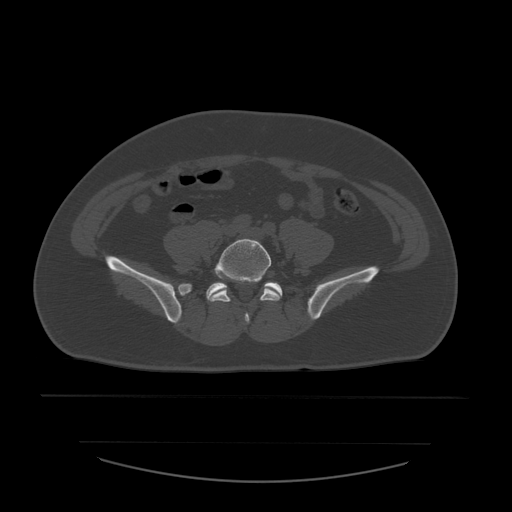
CT including the spine, one axial slice; position 114 of 532 along the scan axis; bone window (W 1800 / L 400 HU); 1.25 mm slice thickness; 512 × 512 image matrix, field of view 441 × 441 mm. Patient age 44 years. Case-level facts recorded for this patient, not image findings: primary cancer: soft tissue sarcoma.
Outlined on this slice (semi-automatically segmented with operator editing):
- L5 vertebra: bounding box [x1, y1, x2, y2] px = [208, 239, 281, 324]